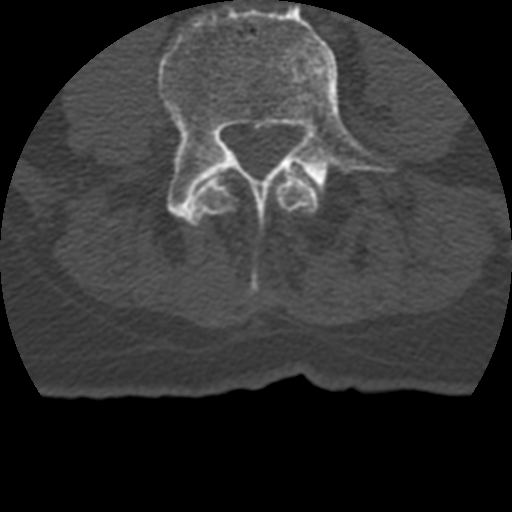
CT including the spine, one axial slice. Position 71 of 399 along the scan axis. 120 kVp. Bone window (W 1800 / L 400 HU). 1.25 mm slice thickness. 512 × 512 image matrix, field of view 160 × 160 mm. Patient age 69 years. From the clinical record (not read from this slice): primary cancer: prostate.
Structures marked on this image (semi-automatic segmentation, software-assisted and operator-edited):
- L3 vertebra: bounding box <194,175,319,293> (left, top, right, bottom; pixels)
- L4 vertebra: <158,4,396,226>